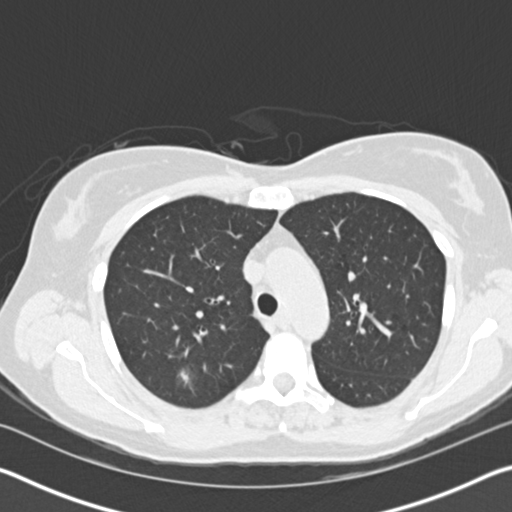
Axial slice from a low-dose chest CT screening exam. Baseline screening round. Lung window (W 1500 / L -600 HU). Standard (soft-tissue) reconstruction kernel (B30f). Slice 48 of 150 in the series. 512 × 512 image matrix, field of view 340 × 340 mm. Female participant, aged 58 years at enrolment. Current smoker at enrolment.
Expert-annotated lung lesion, bounding box <159,354,215,406> (left, top, right, bottom; pixels). The screening reader recorded 3 non-calcified nodules or masses ≥4 mm on this exam (right upper lobe, left upper lobe, left upper lobe); which of them this box marks is not recorded.